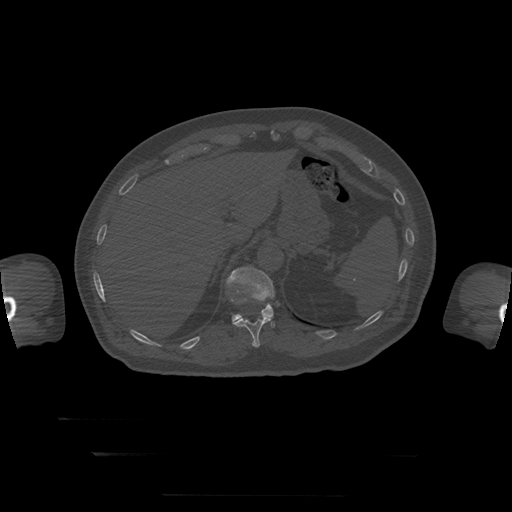
CT including the spine, one axial slice. Position 89 of 397 along the scan axis. Reconstruction kernel STANDARD. 120 kVp. Bone window (W 1800 / L 400 HU). 1.25 mm slice thickness. 512 × 512 image matrix, field of view 510 × 510 mm. Patient age 73 years. From the clinical record (not read from this slice): primary cancer: prostate.
Outlined on this slice (semi-automatically segmented with operator editing):
- T11 vertebra: bounding box <233,312,276,348> (left, top, right, bottom; pixels)
- T12 vertebra: <226,267,275,323>